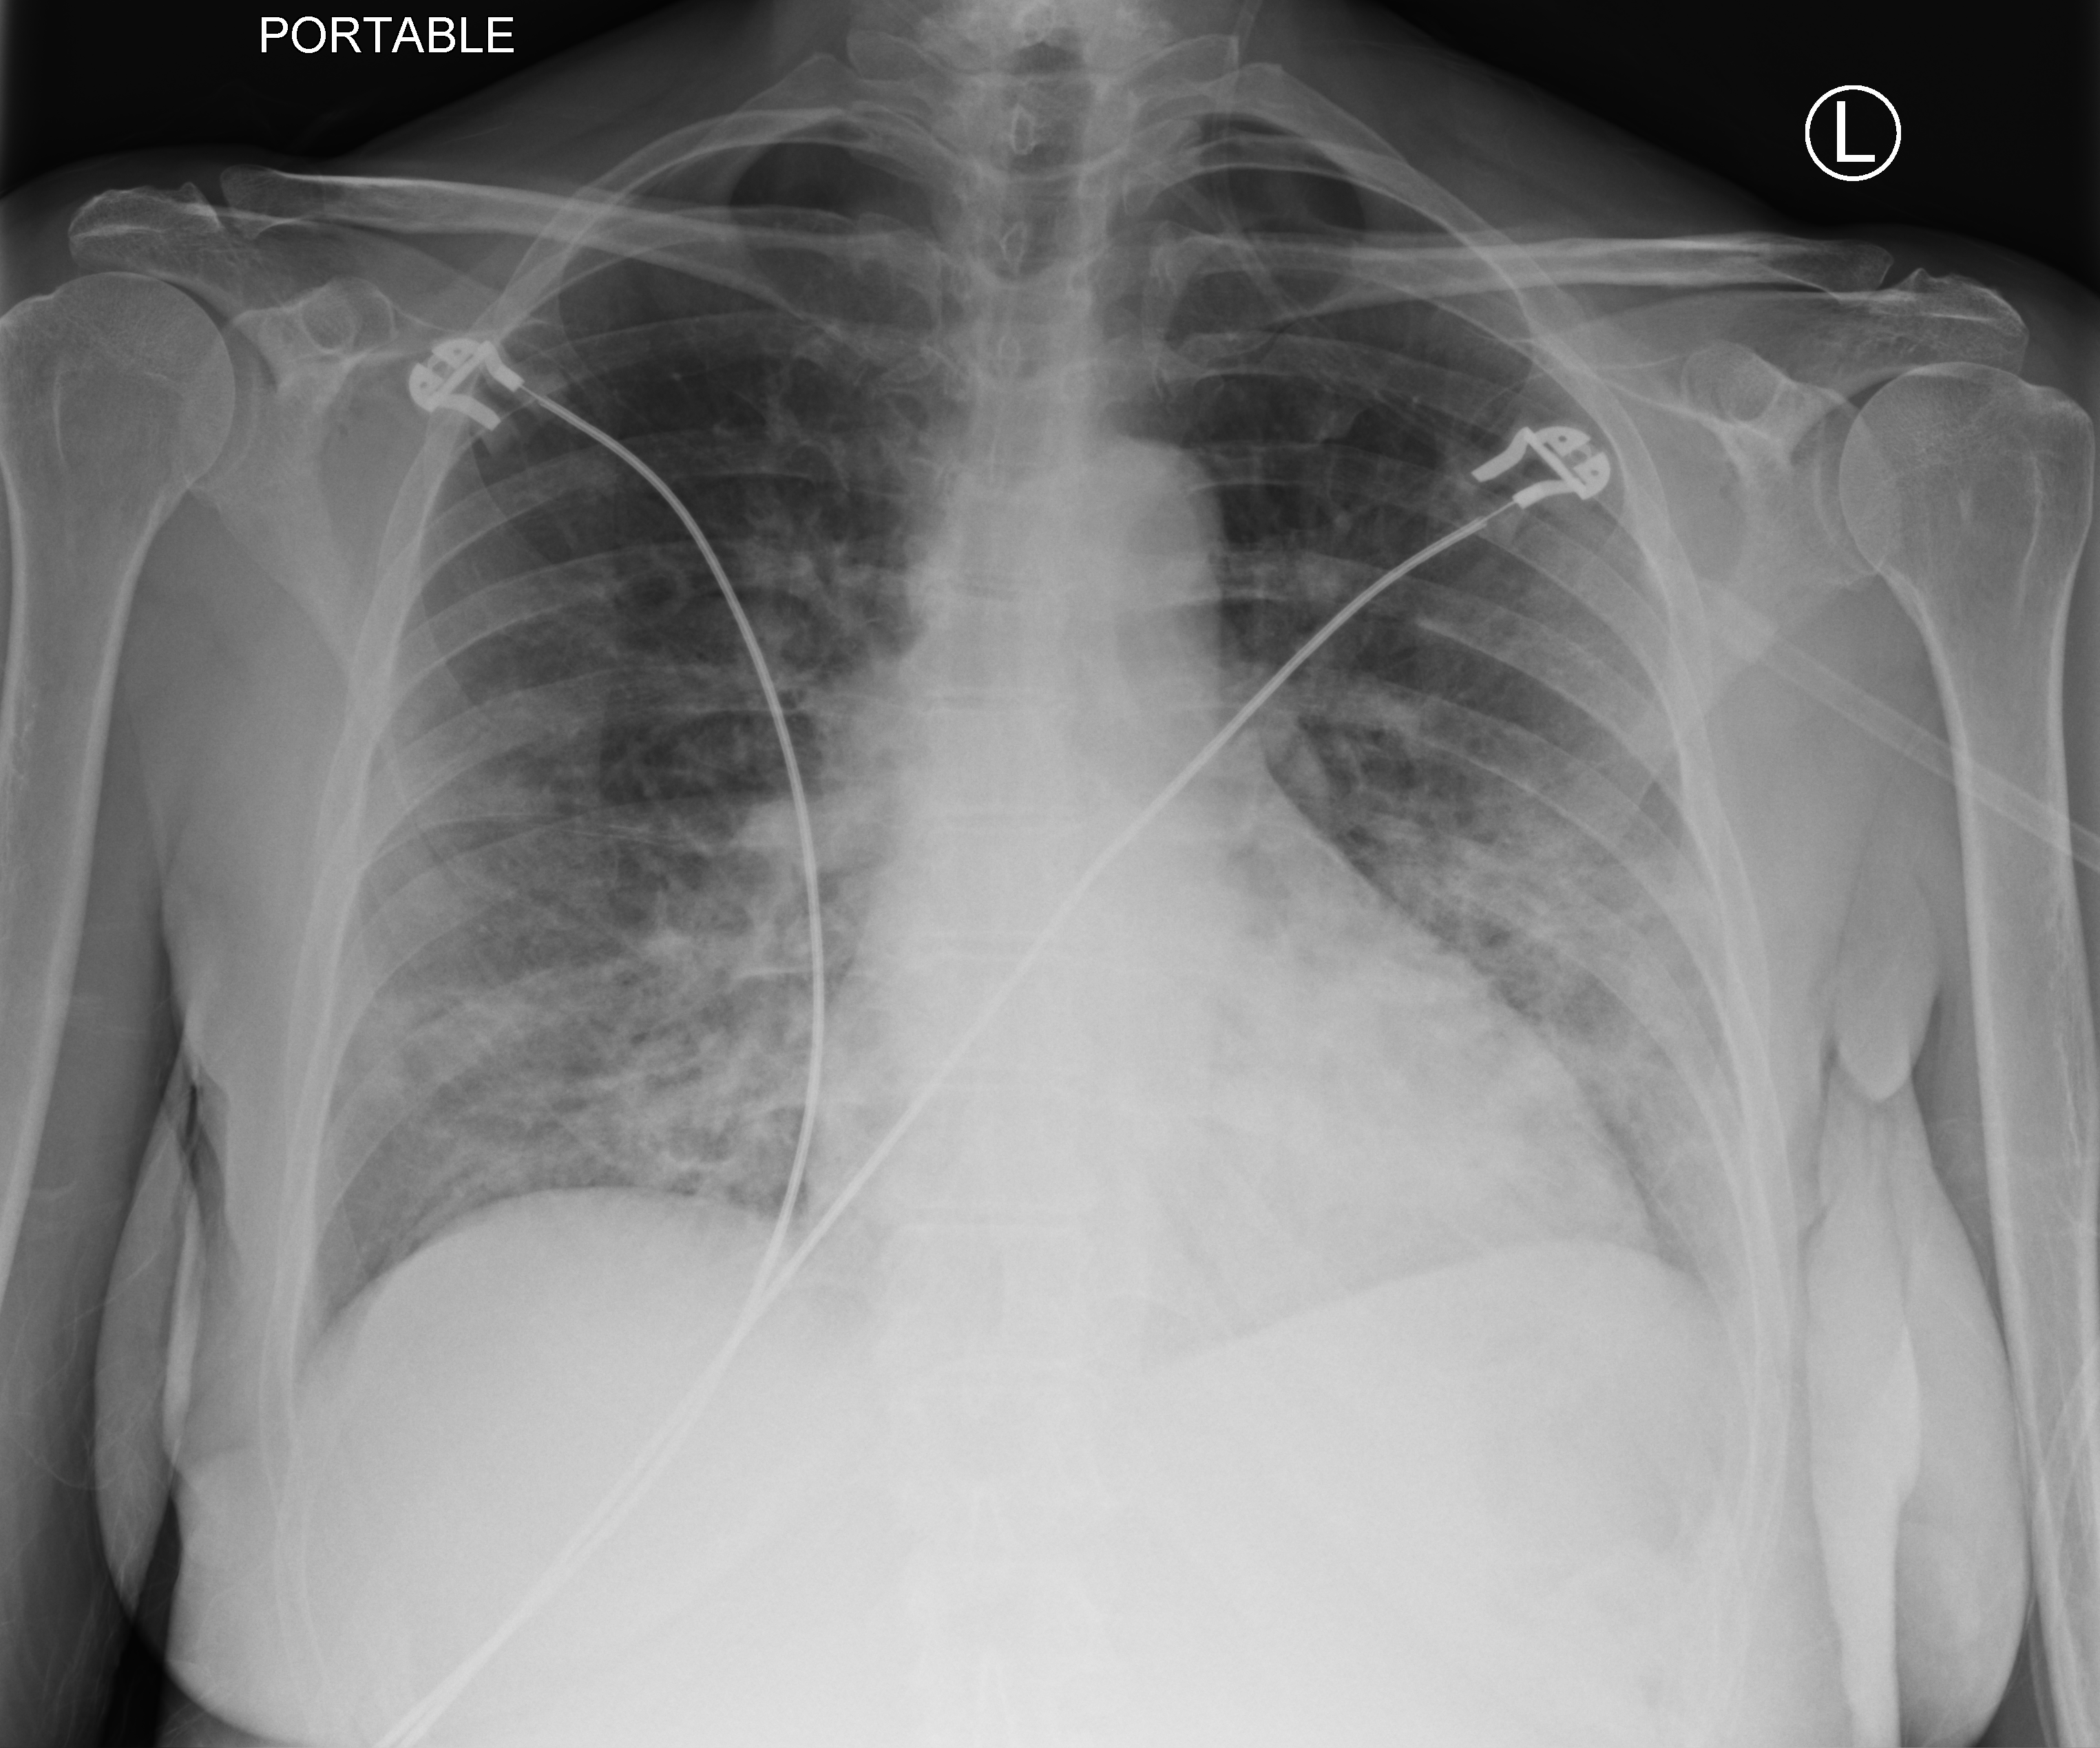
Bedside chest radiograph (computed radiography); anteroposterior (AP) projection. Female patient hospitalised with COVID-19, age 18–59 years.
Hospital-stay facts (about this admission, not read from this image; timing relative to this image not recorded):
- mechanically ventilated during this hospital stay: no
- length of hospital stay: 6 days